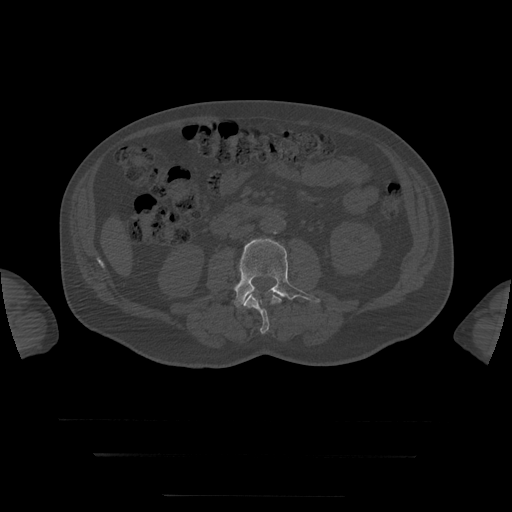
CT including the spine, one axial slice; position 4 of 397 along the scan axis; bone window (W 1800 / L 400 HU); 1.25 mm slice thickness; 512 × 512 image matrix, field of view 510 × 510 mm. Patient age 73 years. From the clinical record (not read from this slice): primary cancer: prostate.
Structures marked on this image (semi-automatic segmentation, software-assisted and operator-edited):
- L3 vertebra: bounding box <234,239,320,307> (left, top, right, bottom; pixels)